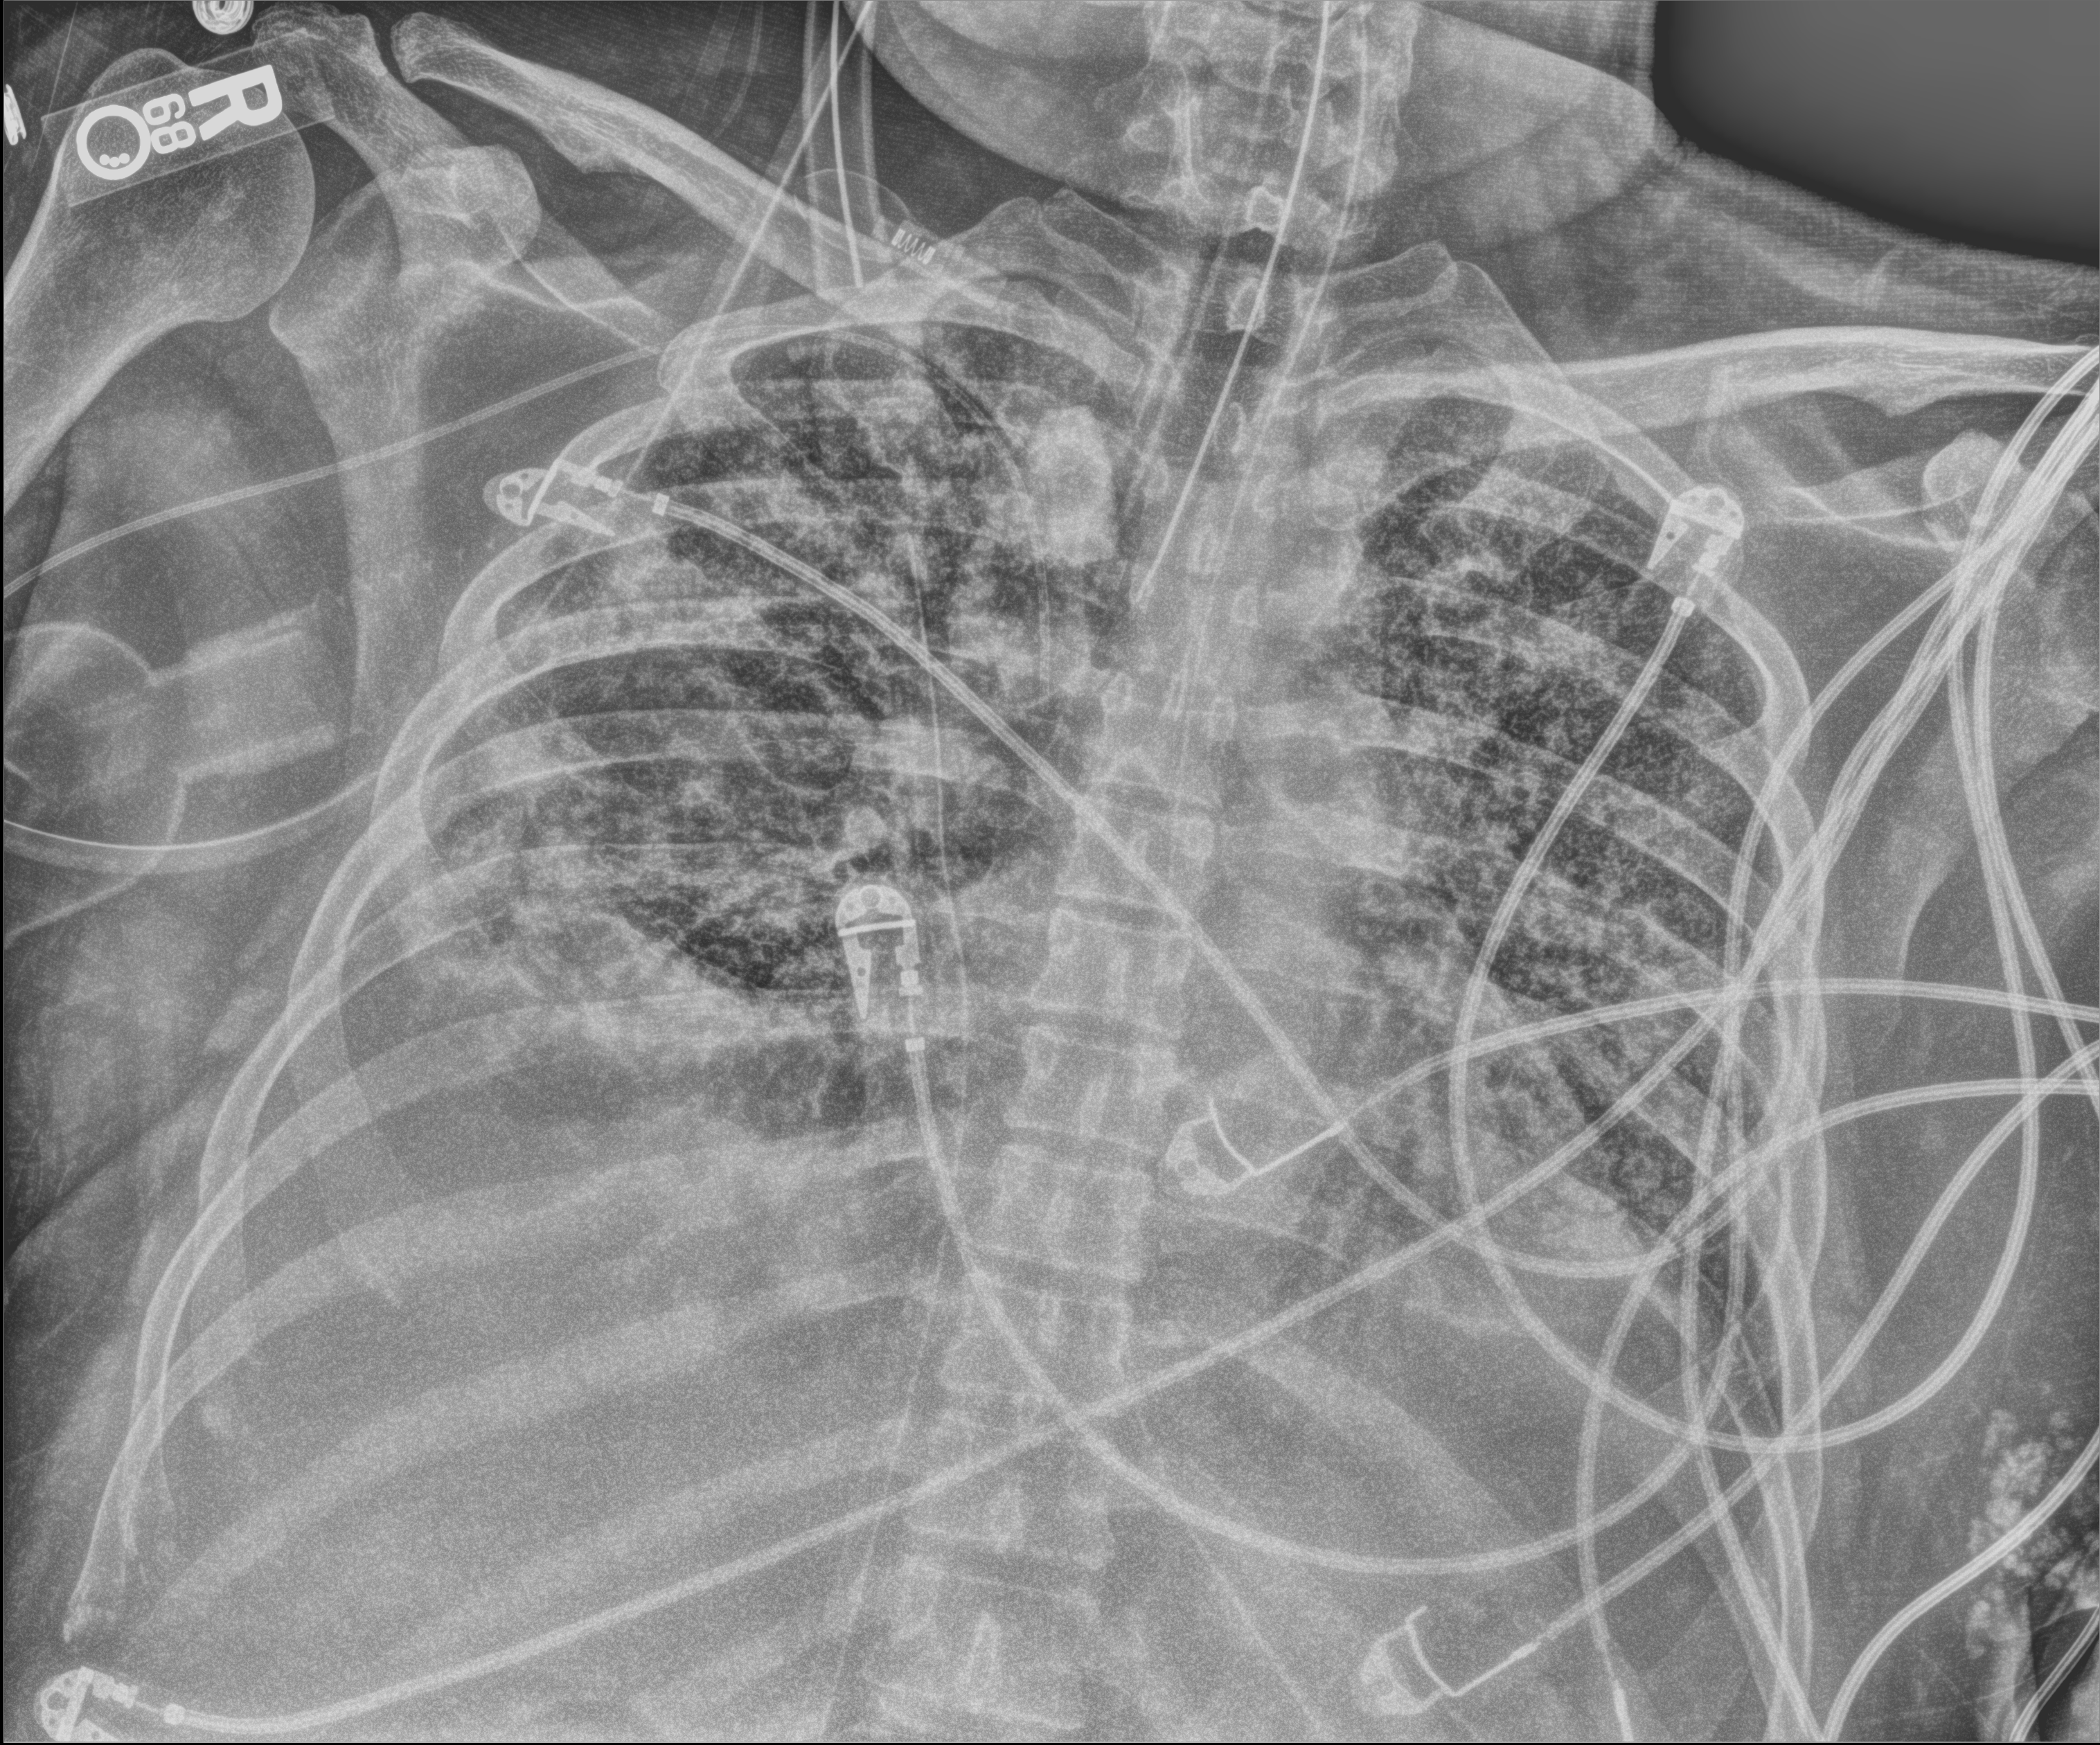
Portable chest radiograph. Male patient hospitalised with COVID-19, age 18–59 years.
Hospital-stay facts (about this admission, not read from this image; timing relative to this image not recorded): admitted to intensive care during this hospital stay: yes; diabetes (admission record): no; mechanically ventilated during this hospital stay: yes.